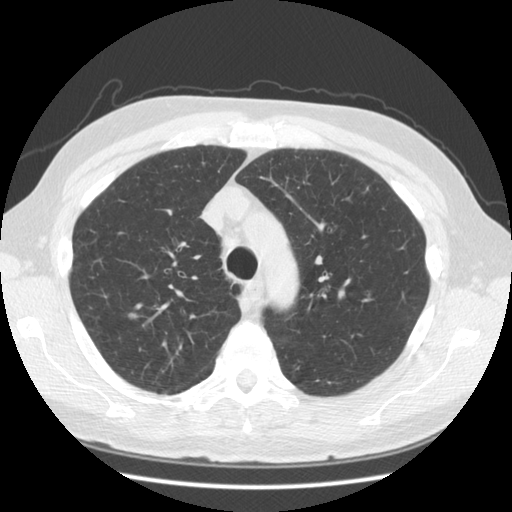
Chest CT (low-dose screening protocol), one axial image. Second annual screen. Lung window (W 1500 / L -600 HU). 2.5 mm slice thickness. Standard (soft-tissue) reconstruction kernel (STANDARD). Slice 116 of 155 in the series. 512 × 512 image matrix, field of view 350 × 350 mm. Male participant, aged 68 years at enrolment. Current smoker at enrolment.
- Expert reader's lesion annotation, box from (x=110, y=295) to (x=155, y=337) px.
- Screening reader's record for this exam: no non-calcified nodule ≥4 mm recorded.
- Official screen result: negative screen, minor abnormalities not suspicious for lung cancer.
- Later outcome: lung cancer diagnosed 596 days after this screen (after the third annual screen) — adenocarcinoma, NOS, right upper lobe, moderately differentiated (G2), stage IA (AJCC 6th edition), 13 mm at pathology.